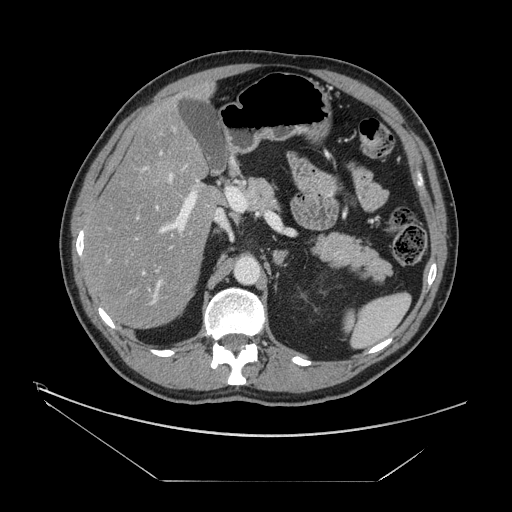
Contrast-enhanced abdominal CT, one axial slice; reconstruction kernel STANDARD; intravenous contrast given; soft-tissue window (W 400 / L 40 HU); 2.5 mm slice thickness; 512 × 512 image matrix, field of view 440 × 440 mm. Male patient, age 65 years. Case-level facts recorded for this patient, not image findings: diagnosis: colorectal cancer liver metastases, imaged before liver resection; multiple liver metastases: yes; largest metastasis: 4.2 cm; disease in both lobes: yes.
Annotated regions visible in this slice (manually delineated by an expert):
- hepatic veins: box from (x=135, y=164) to (x=187, y=291) px
- liver: (x=86, y=87)–(x=221, y=329)
- planned liver remnant (the part of the liver to remain after resection): (x=98, y=89)–(x=219, y=329)
- portal vein (with intrahepatic branches): (x=112, y=152)–(x=203, y=325)